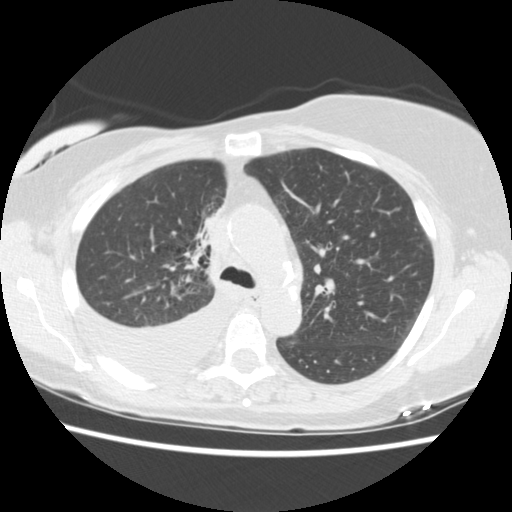
Axial slice from a low-dose chest CT screening exam; third screening round (two years after baseline); lung window (W 1500 / L -600 HU); 2.5 mm slice thickness; standard (soft-tissue) reconstruction kernel (STANDARD); slice 55 of 157 in the series. Female, age 56 years at enrolment. Current smoker at enrolment.
- Lesion marked by an expert reader, bounding box [x1, y1, x2, y2] px = [180, 191, 238, 256].
- The screening reader recorded 2 non-calcified nodules or masses ≥4 mm on this exam; which of them this box marks is not recorded.
- Official screen result: positive, other.